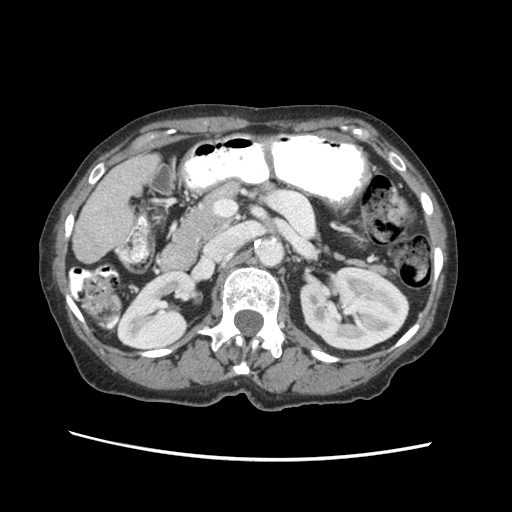
Contrast-enhanced abdominal CT (liver protocol), one axial slice; position 16 of 63 along the scan axis; reconstruction kernel STANDARD; soft-tissue window (W 400 / L 40 HU); 2.5 mm slice thickness; 512 × 512 image matrix, field of view 340 × 340 mm. From the clinical record (not read from this slice): diagnosis: hepatocellular carcinoma (patient treated with transarterial chemoembolisation; whether this scan precedes or follows treatment is not stated here); TNM stage (as recorded): Stage-I; Child-Pugh class: B; tumour nodularity: uninodular.
Structures marked on this image (semi-automatically segmented with operator editing):
- liver parenchyma outside the tumour (the mass and vessels are separate outlines, so this box may not span the whole liver): box from (x=72, y=152) to (x=156, y=262) px